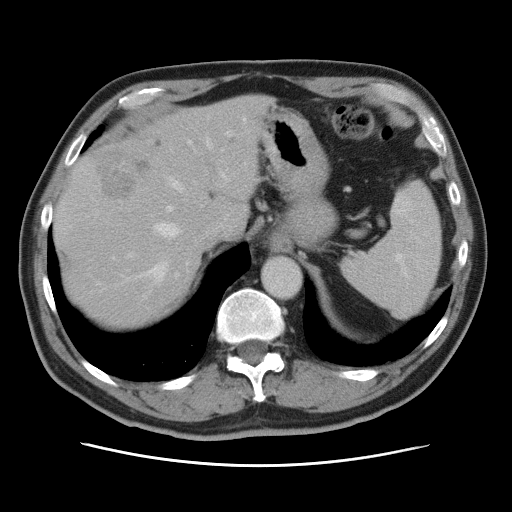
Contrast-enhanced abdominal CT, one axial slice. Intravenous contrast given. Soft-tissue window (W 400 / L 40 HU). 5 mm slice thickness. 512 × 512 image matrix, field of view 370 × 370 mm. Male patient, age 69 years. From the clinical record (not read from this slice): diagnosis: colorectal cancer liver metastases, imaged before liver resection; multiple liver metastases: no; largest metastasis: 5 cm.
Outlined on this slice (manually delineated by an expert):
- hepatic veins: box from (x=140, y=138) to (x=212, y=283) px
- liver: (x=56, y=95)–(x=269, y=329)
- planned liver remnant (the part of the liver to remain after resection): (x=55, y=95)–(x=269, y=329)
- portal vein (with intrahepatic branches): (x=127, y=129)–(x=234, y=276)
- liver metastasis: (x=98, y=147)–(x=150, y=199)